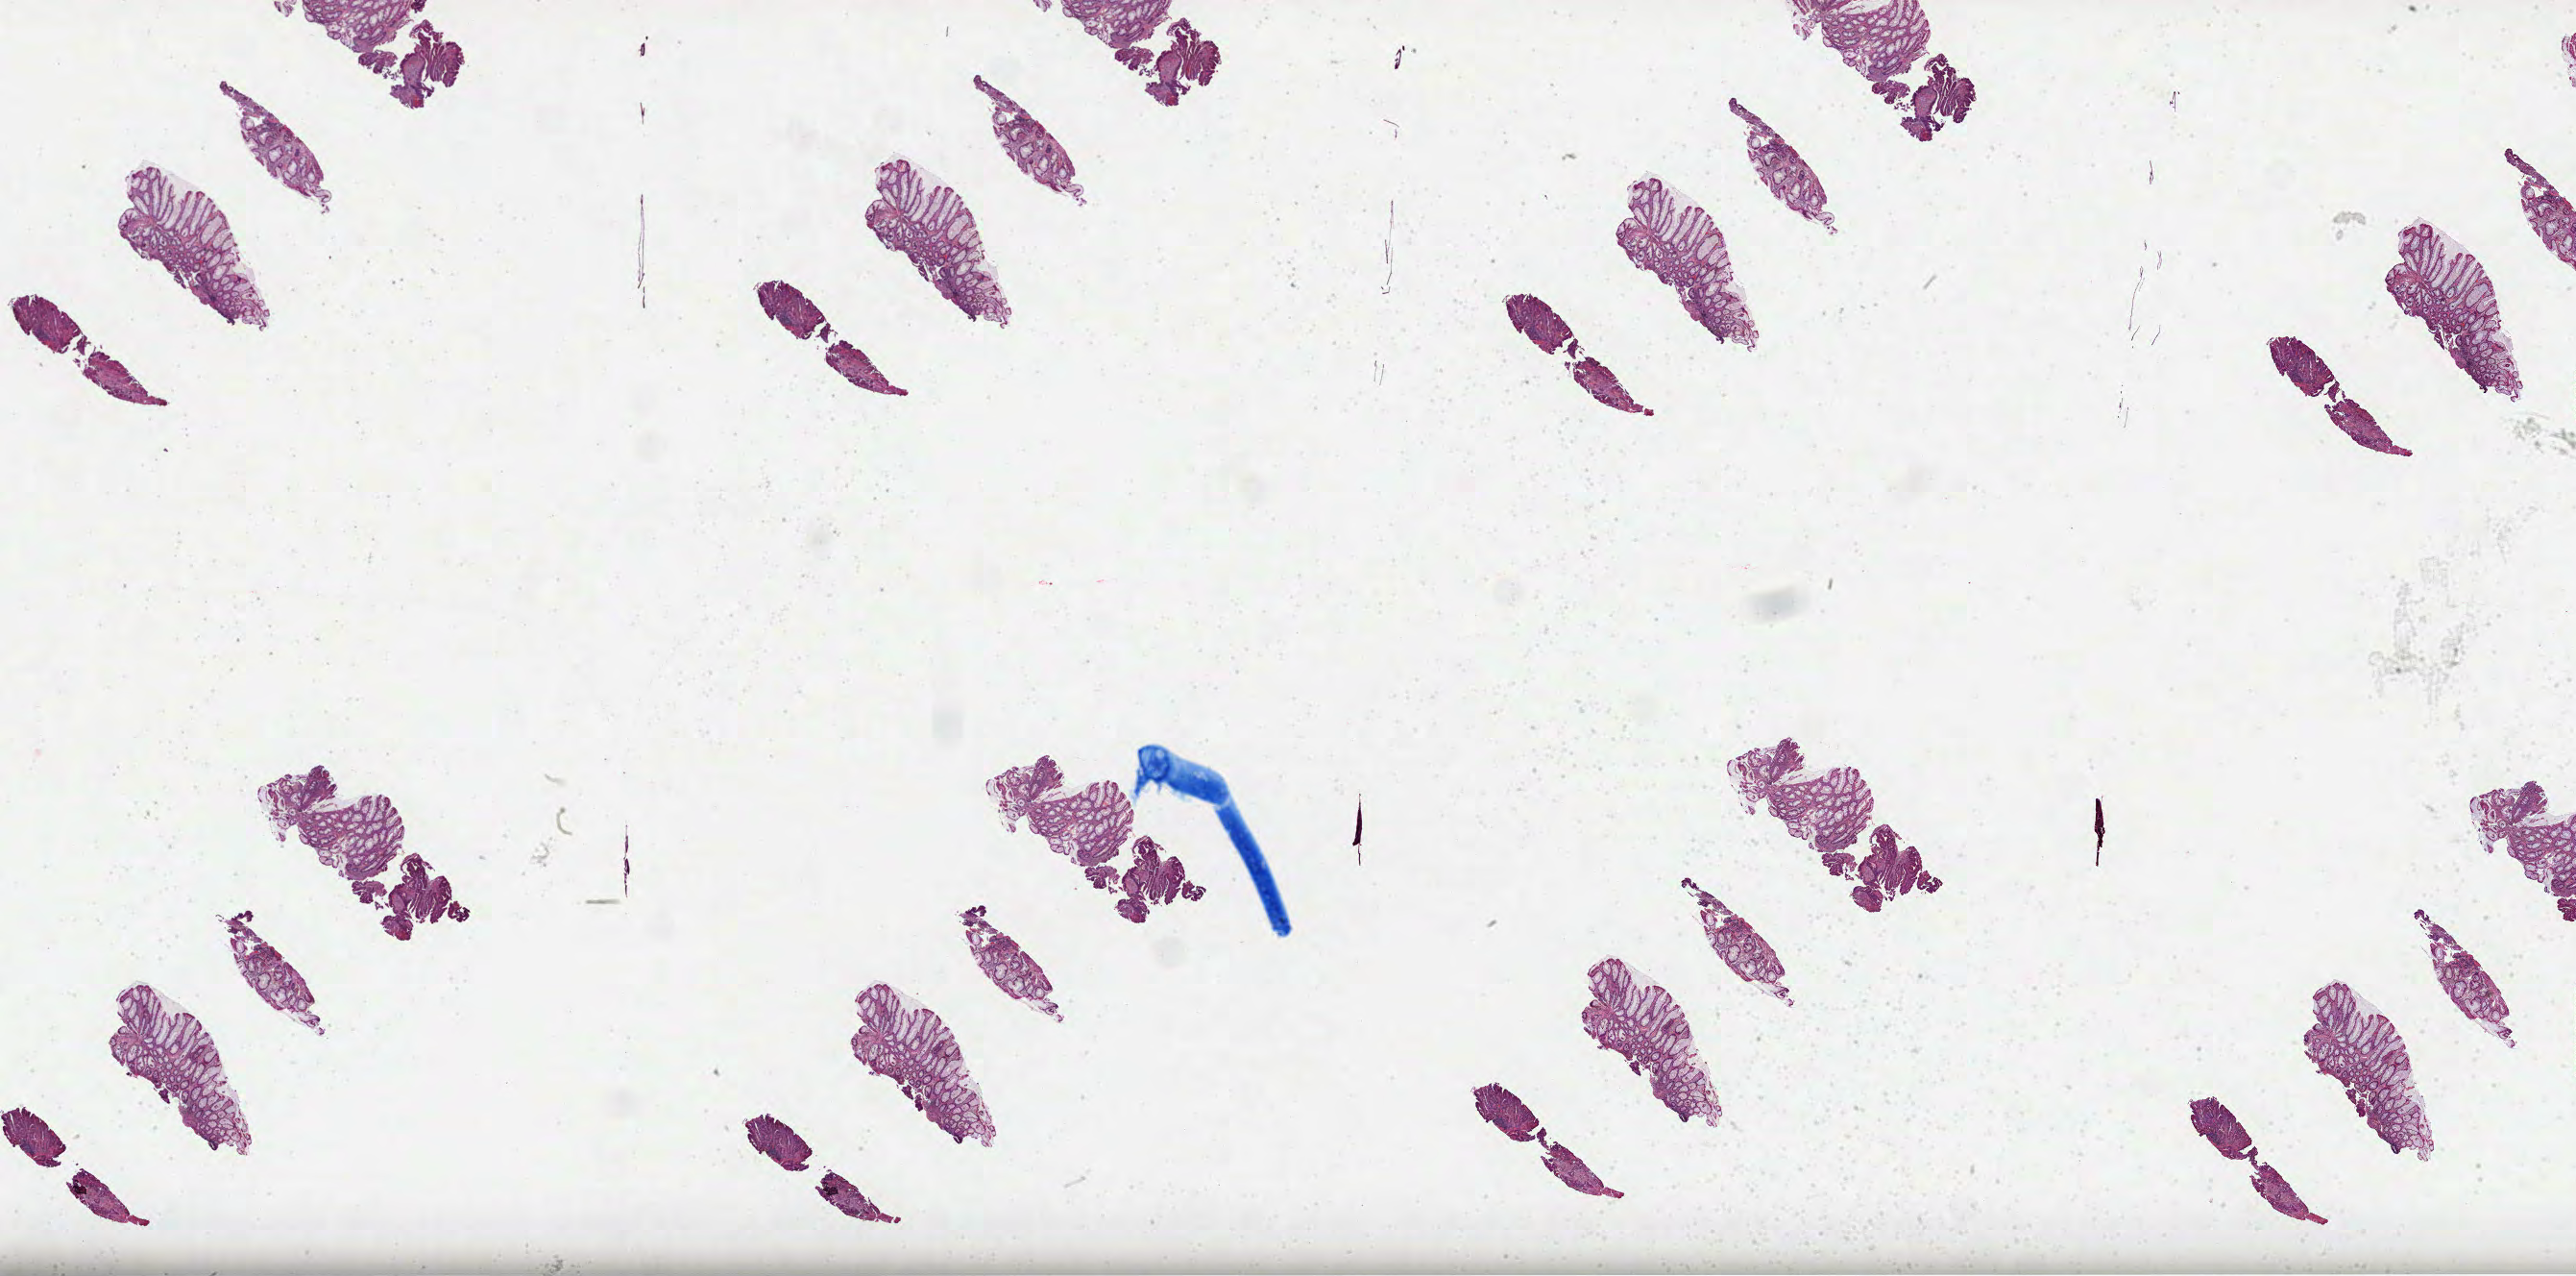
Digitized Hematoxylin and eosin (H&E) stained tissue section (whole slide) — shown as a low-resolution overview of the whole scanned area (about 43.3 x 21.4 mm, acquisition: 40x scan), formalin-fixed paraffin-embedded (FFPE) diagnostic section, sample: primary tumour, rectum. Patient: female, age at initial diagnosis 53 years.
Histologic diagnosis: Adenocarcinoma, NOS. AJCC pathologic stage: I.